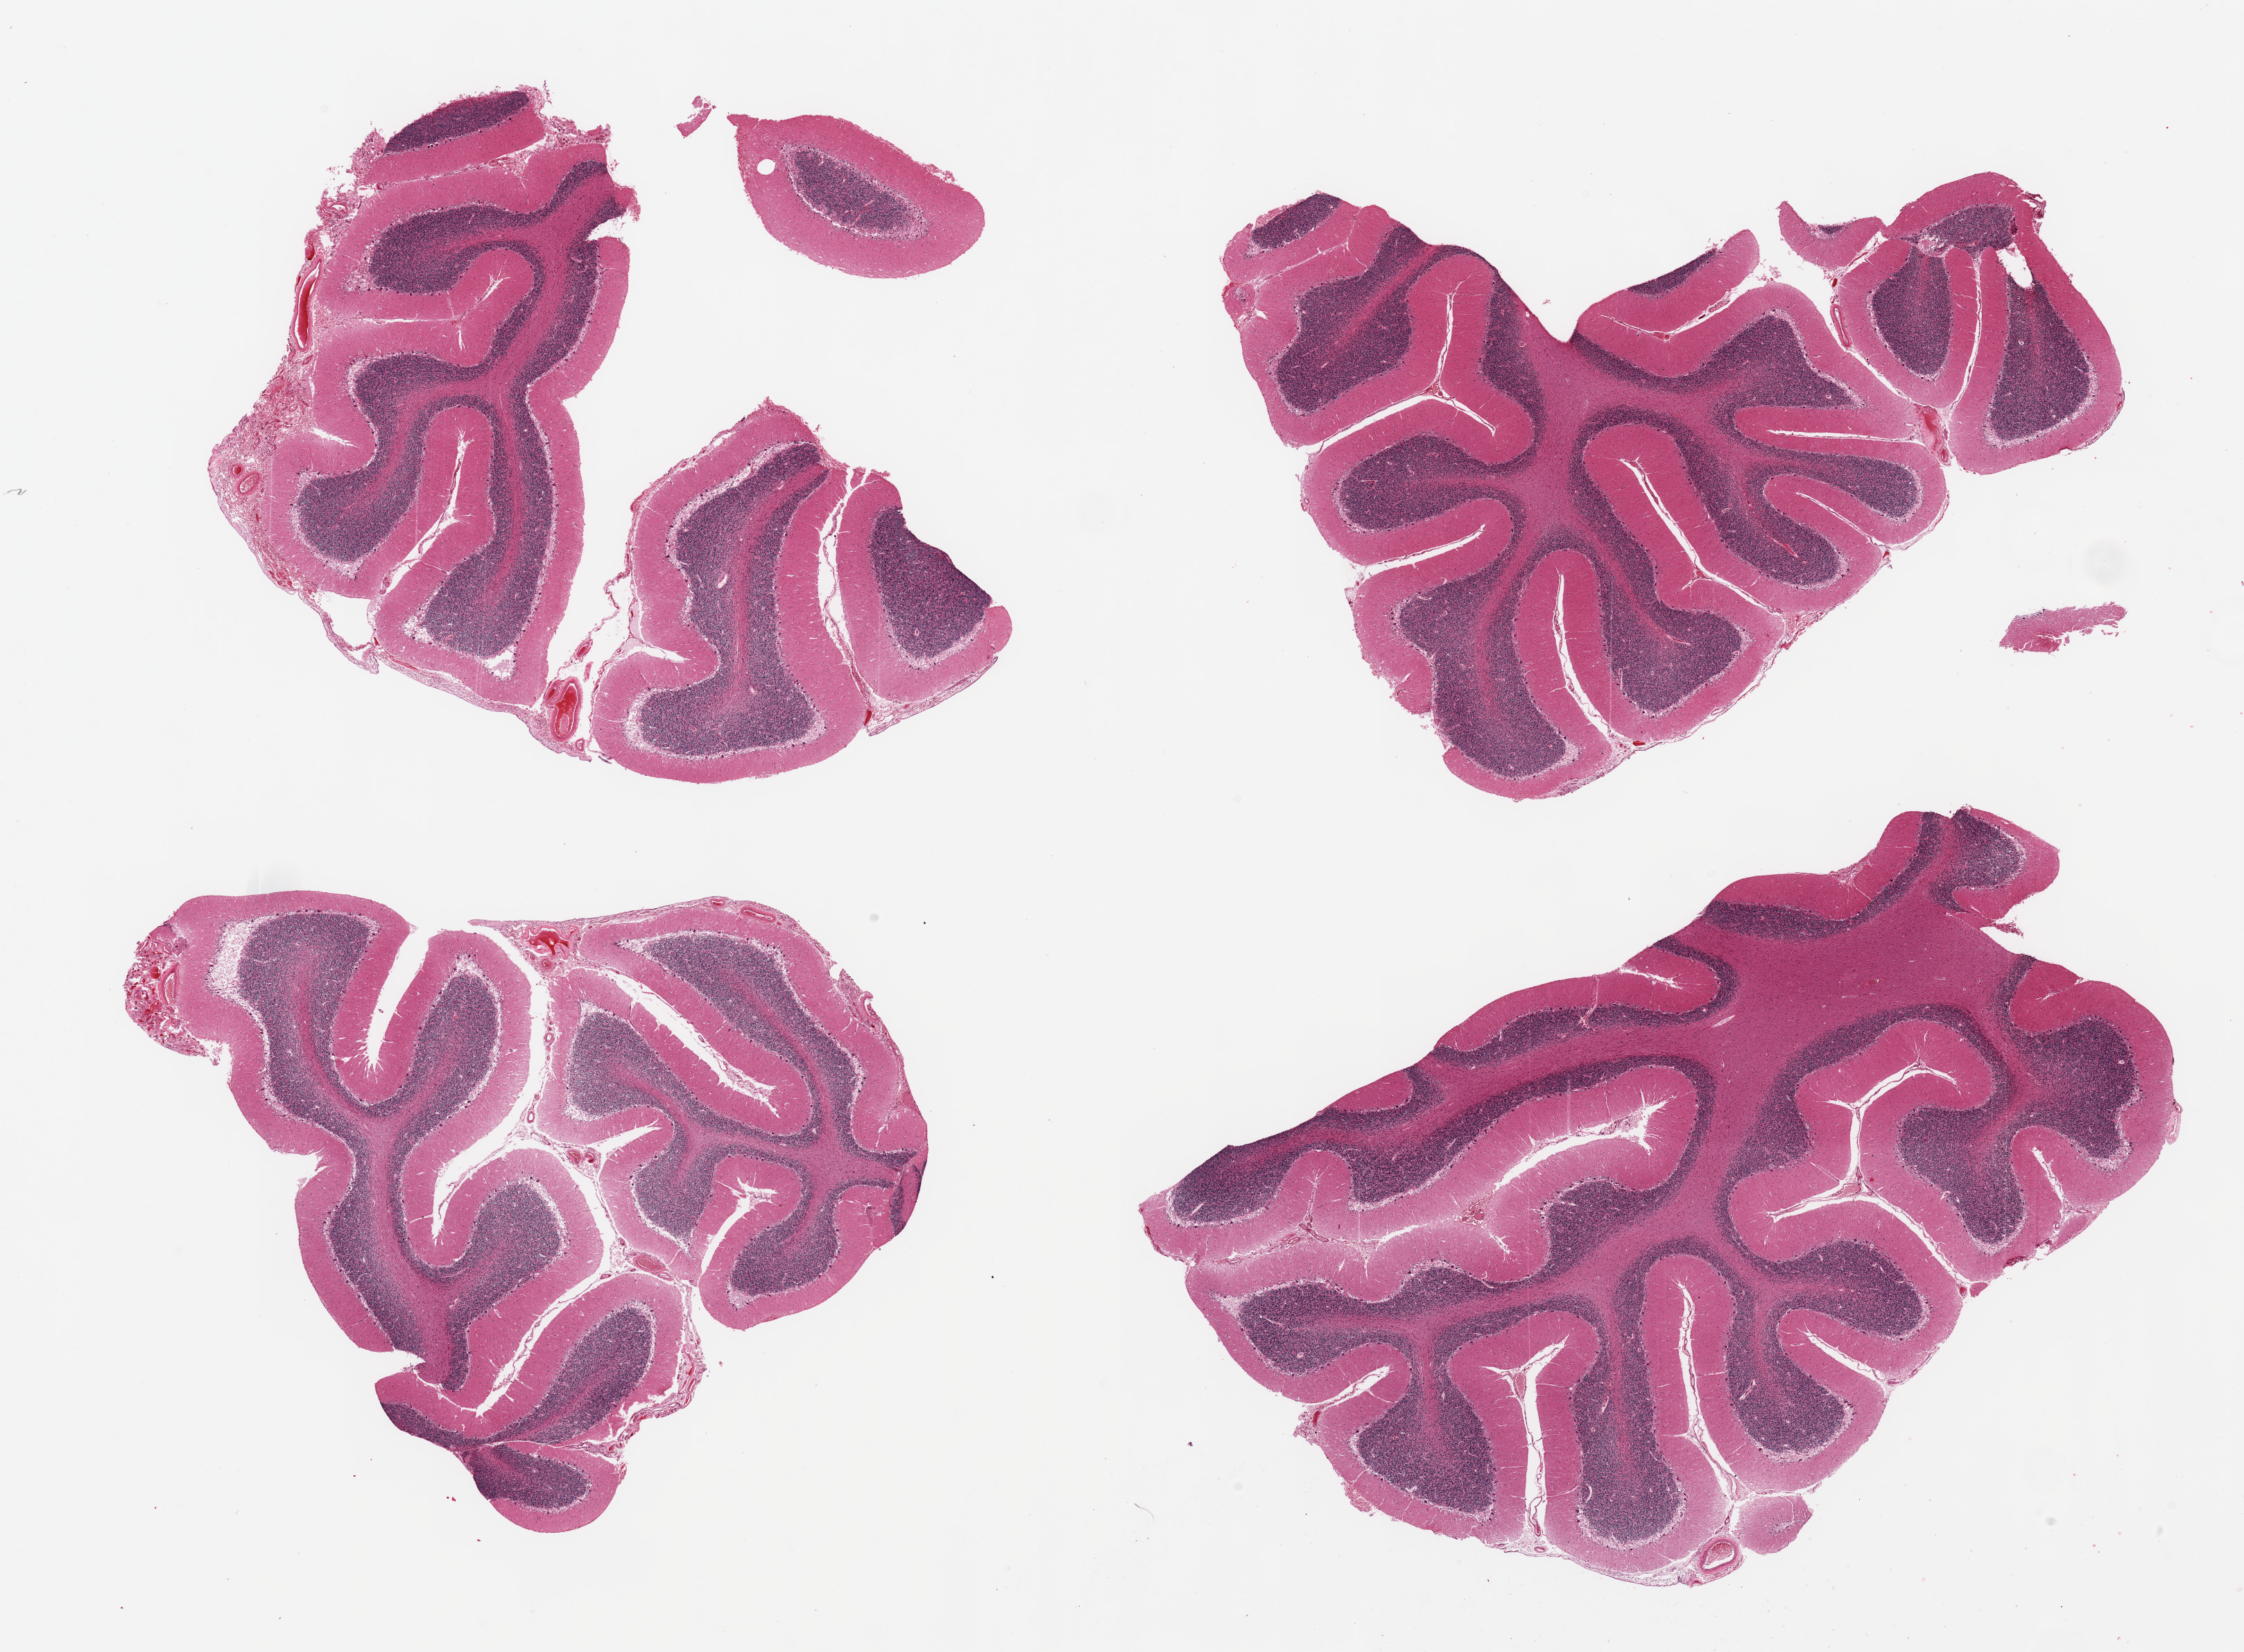
Digitized haematoxylin and eosin-stained section, brightfield — shown as a low-resolution overview of the whole scanned area (about 25.6 x 18.8 mm), PAXgene-fixed, paraffin-embedded tissue, sampled site (target tissue): cerebellum, tissue donor sample. Donor: male.
Reviewer comment on this tissue sample: 4 pieces, no abnormalities.